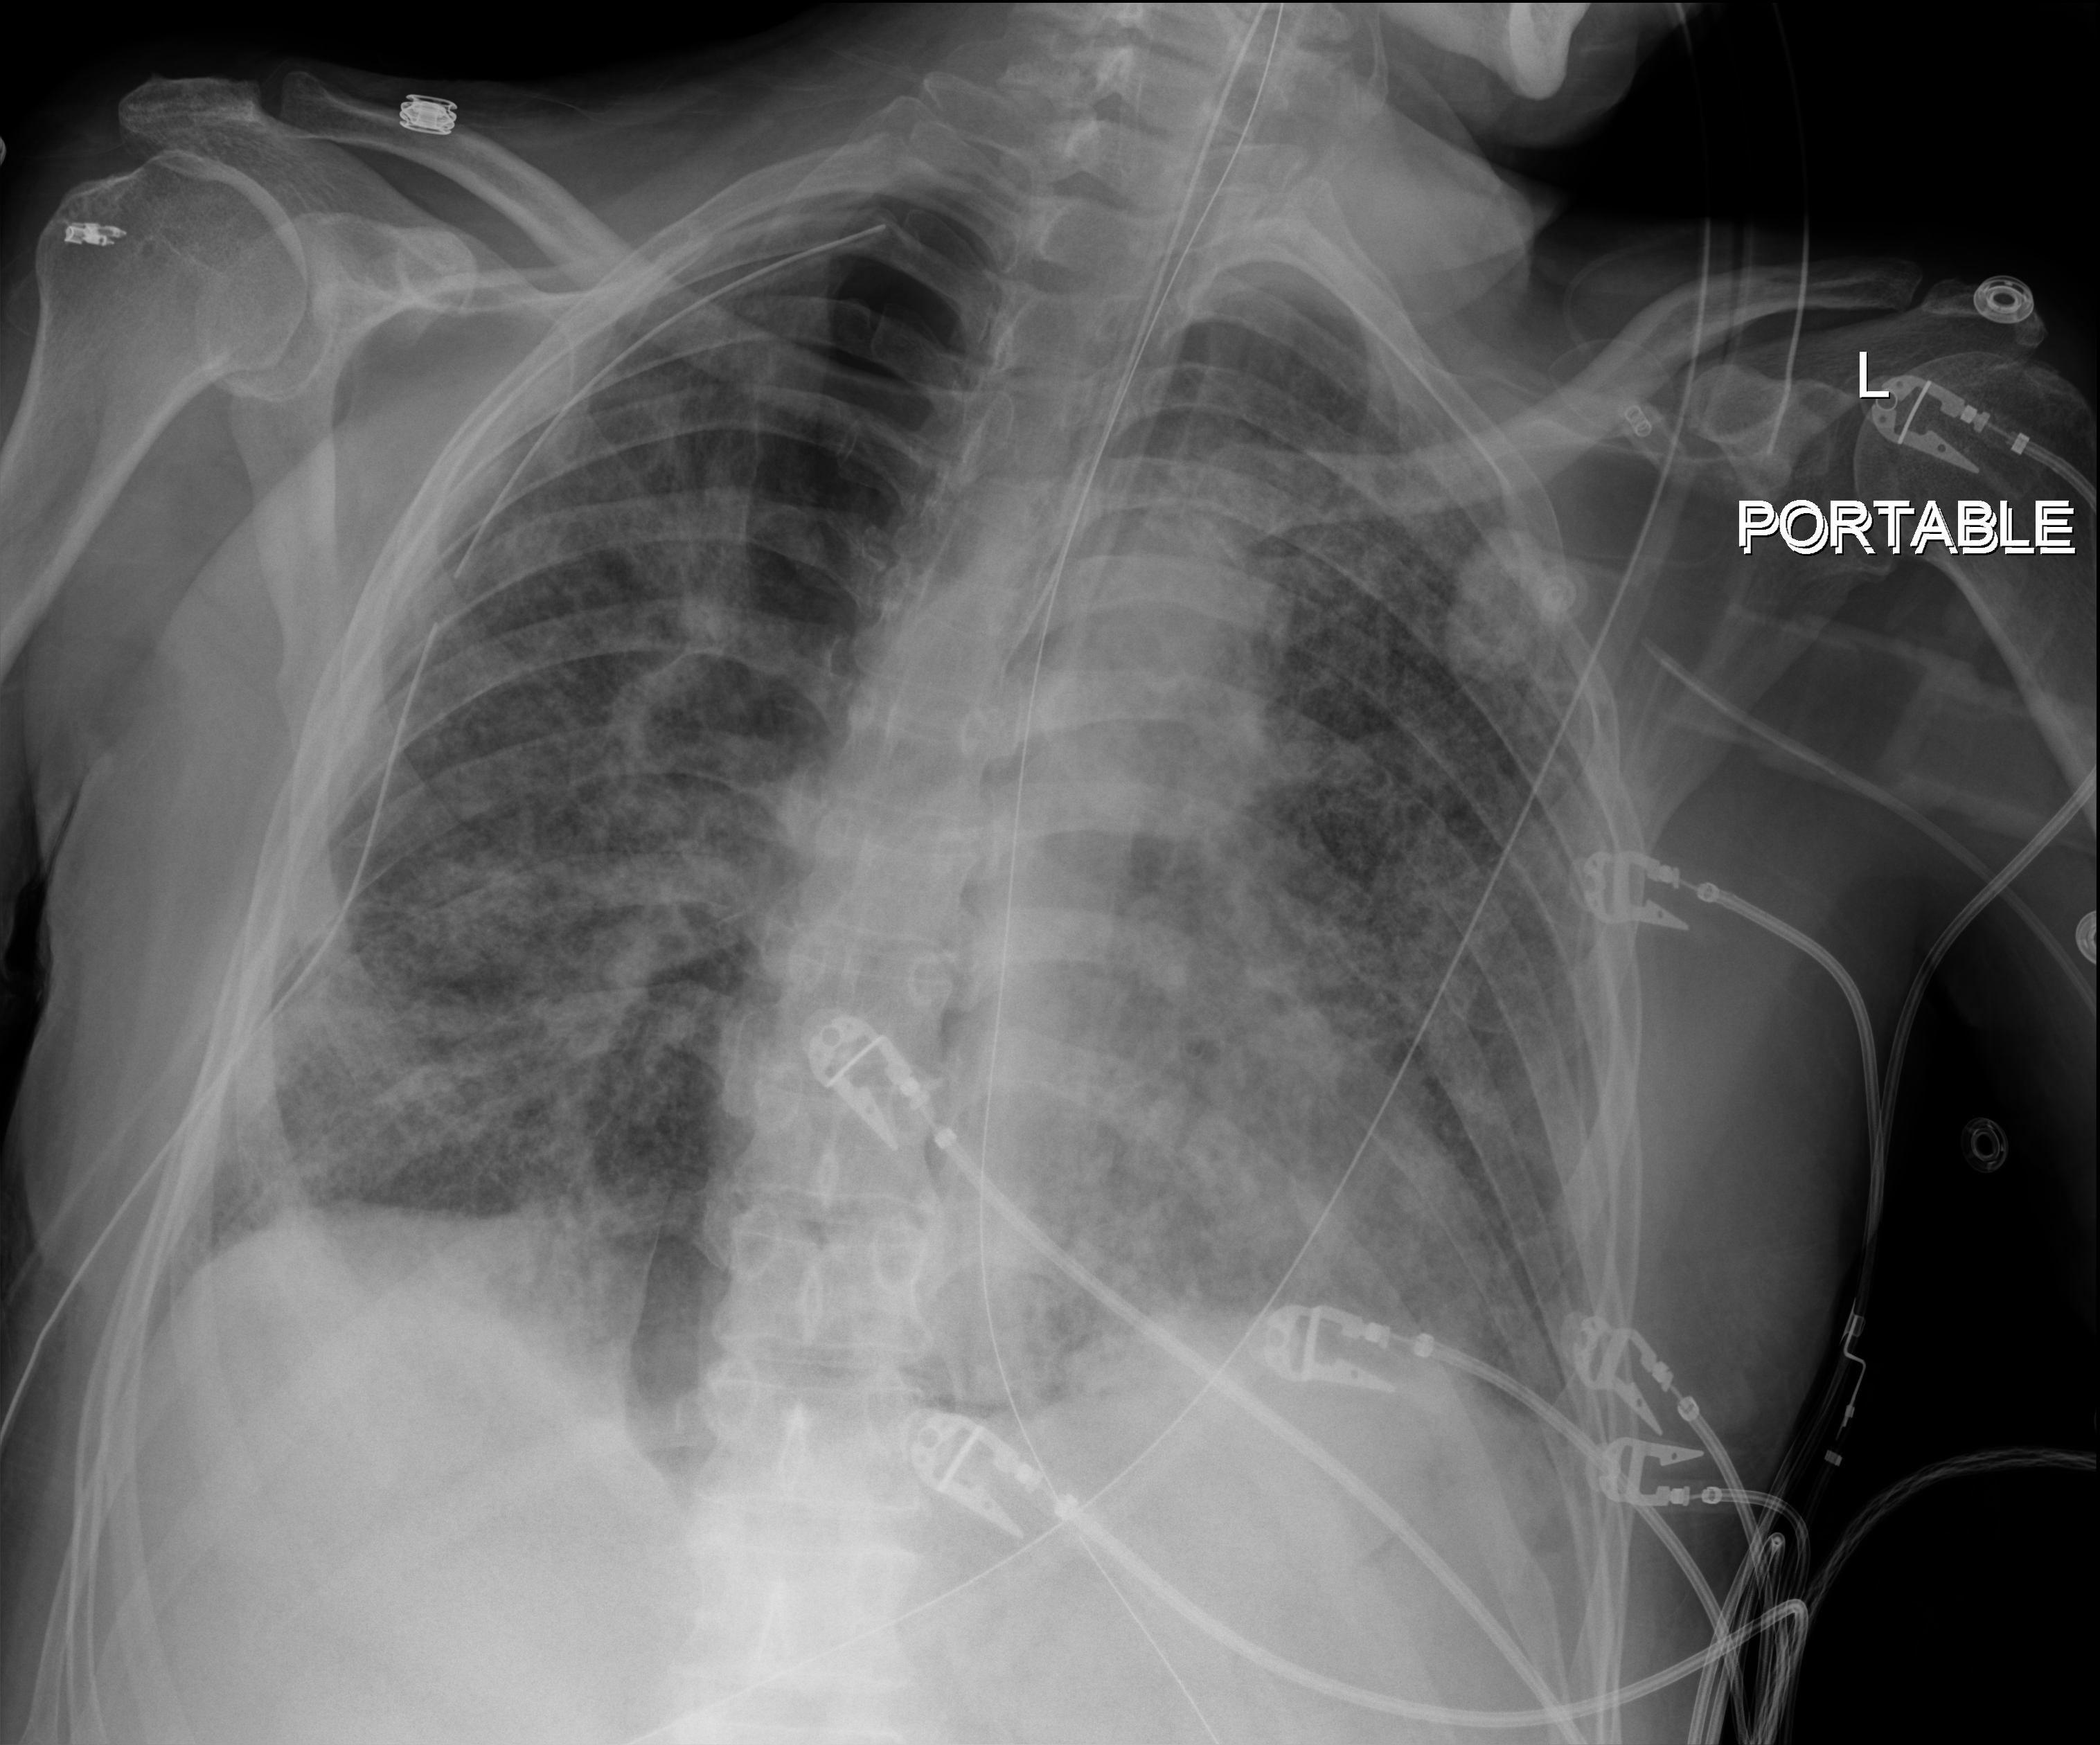
Portable chest radiograph; anteroposterior (AP) projection. Male patient hospitalised with COVID-19, age 60–74 years.
From the hospital-stay record, not from the radiograph (when in the stay this image was taken is not recorded):
- admitted to intensive care during this hospital stay: yes
- length of hospital stay: 65 days